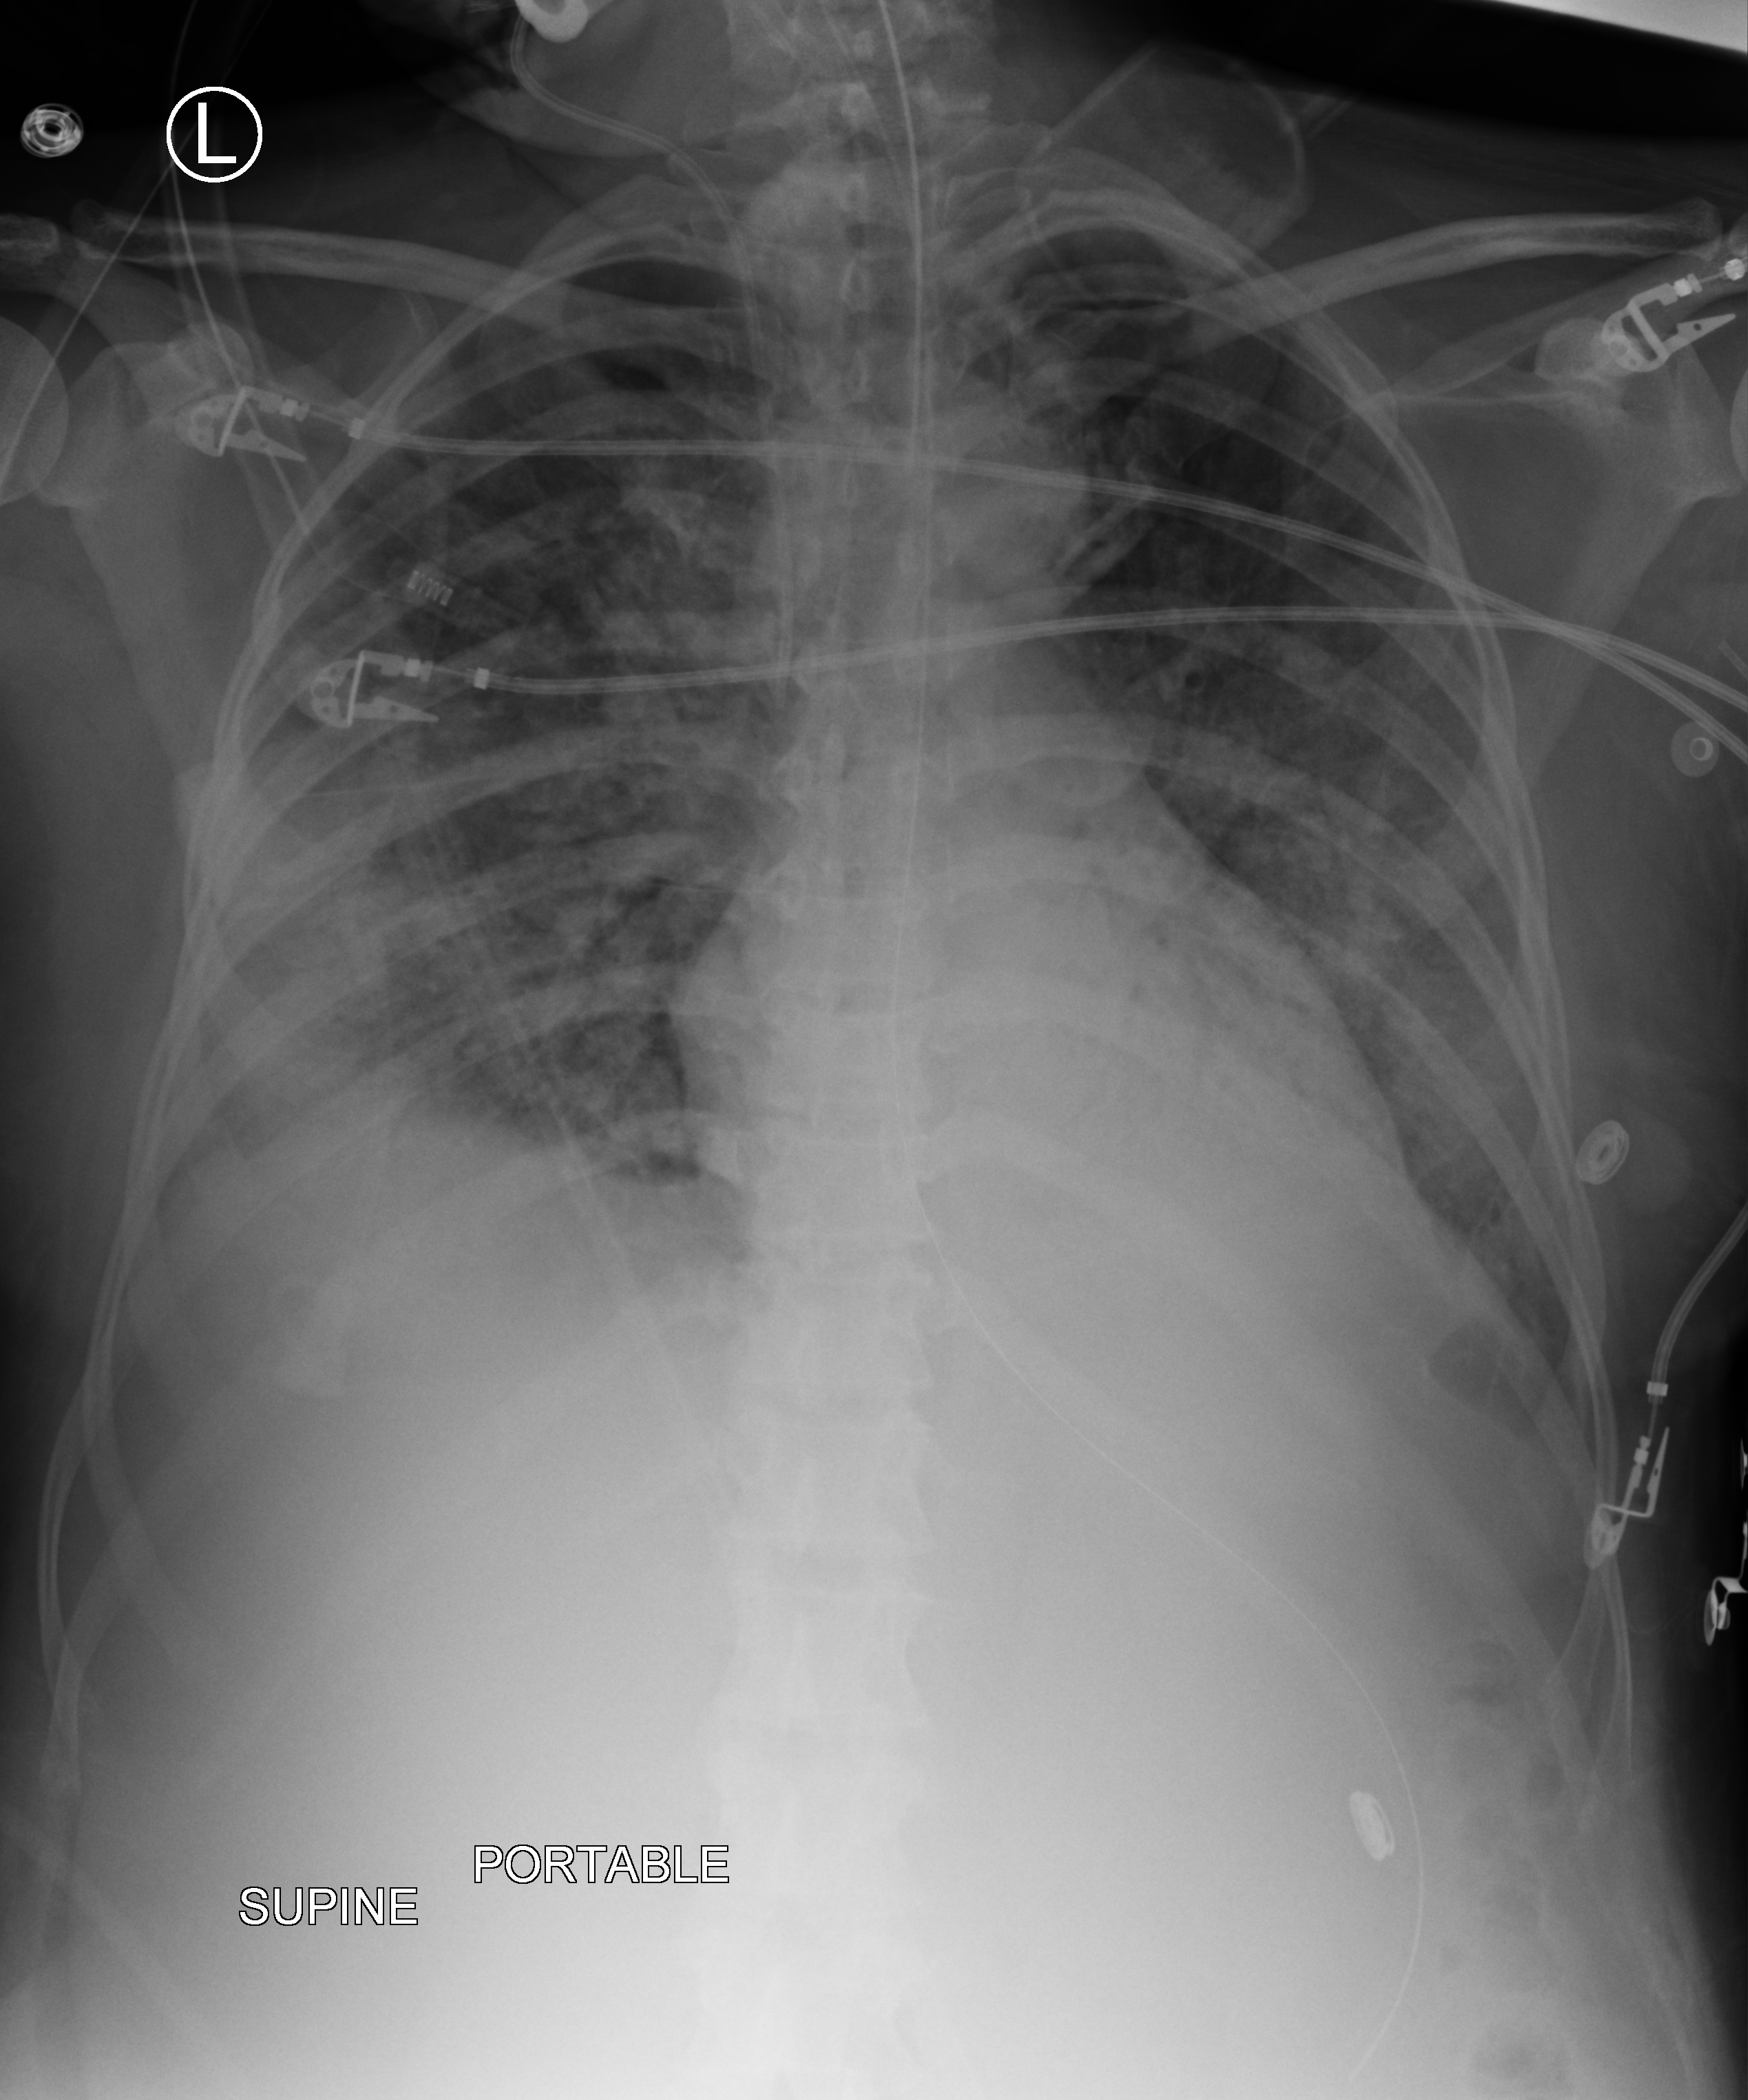
Bedside chest radiograph (computed radiography); anteroposterior (AP) projection. Female patient hospitalised with COVID-19, age 18–59 years.
Admission-level facts for this patient (not findings on this image; timing relative to this image not recorded): admitted to intensive care during this hospital stay: yes; other chronic lung disease (admission record): no; mechanically ventilated during this hospital stay: yes.